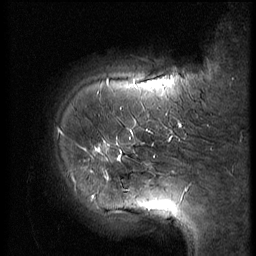
Breast MRI (dynamic contrast-enhanced), one sagittal slice. 3 images stored at this slice position (order not interpretable as contrast timing). 1.5 T. TE 4.2 ms, TR 9 ms. 2.5 mm slice thickness. 256 × 256 image matrix, field of view 180 × 180 mm. Patient: female, 61 years. Case-level facts recorded for this patient, not image findings: setting: breast cancer imaged before/during neoadjuvant chemotherapy; receptor status: HR-positive, HER2-negative.
Structures marked on this image (semi-automatic segmentation, software-assisted and operator-edited):
- analysis volume of interest (the breast-tissue region the enhancement analysis was run in; not a lesion): bounding box [x1, y1, x2, y2] px = [49, 89, 153, 191]
- tumour enhancement mask (voxels above the 140 % enhancement threshold inside the analysis volume of interest): [96, 148, 121, 173]